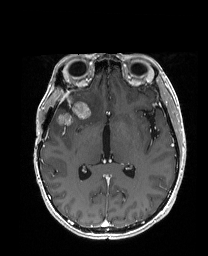
Brain MRI from a brain-tumour surgery series, one axial slice. Slice 95 of 192 in the series (ordered by position). T1-weighted post-contrast. 1 mm slice thickness. 208 × 256 image matrix, field of view 203 × 250 mm. From the clinical record (not read from this slice): histopathology: Metastatic Carcinoma from Breast primary; tumour location: Right Frontal.
Annotated regions visible in this slice (expert manual segmentation):
- previous resection cavity: bounding box (x1, y1, x2, y2) in pixels: (60, 102, 71, 112)
- tumour: (55, 95, 104, 125)